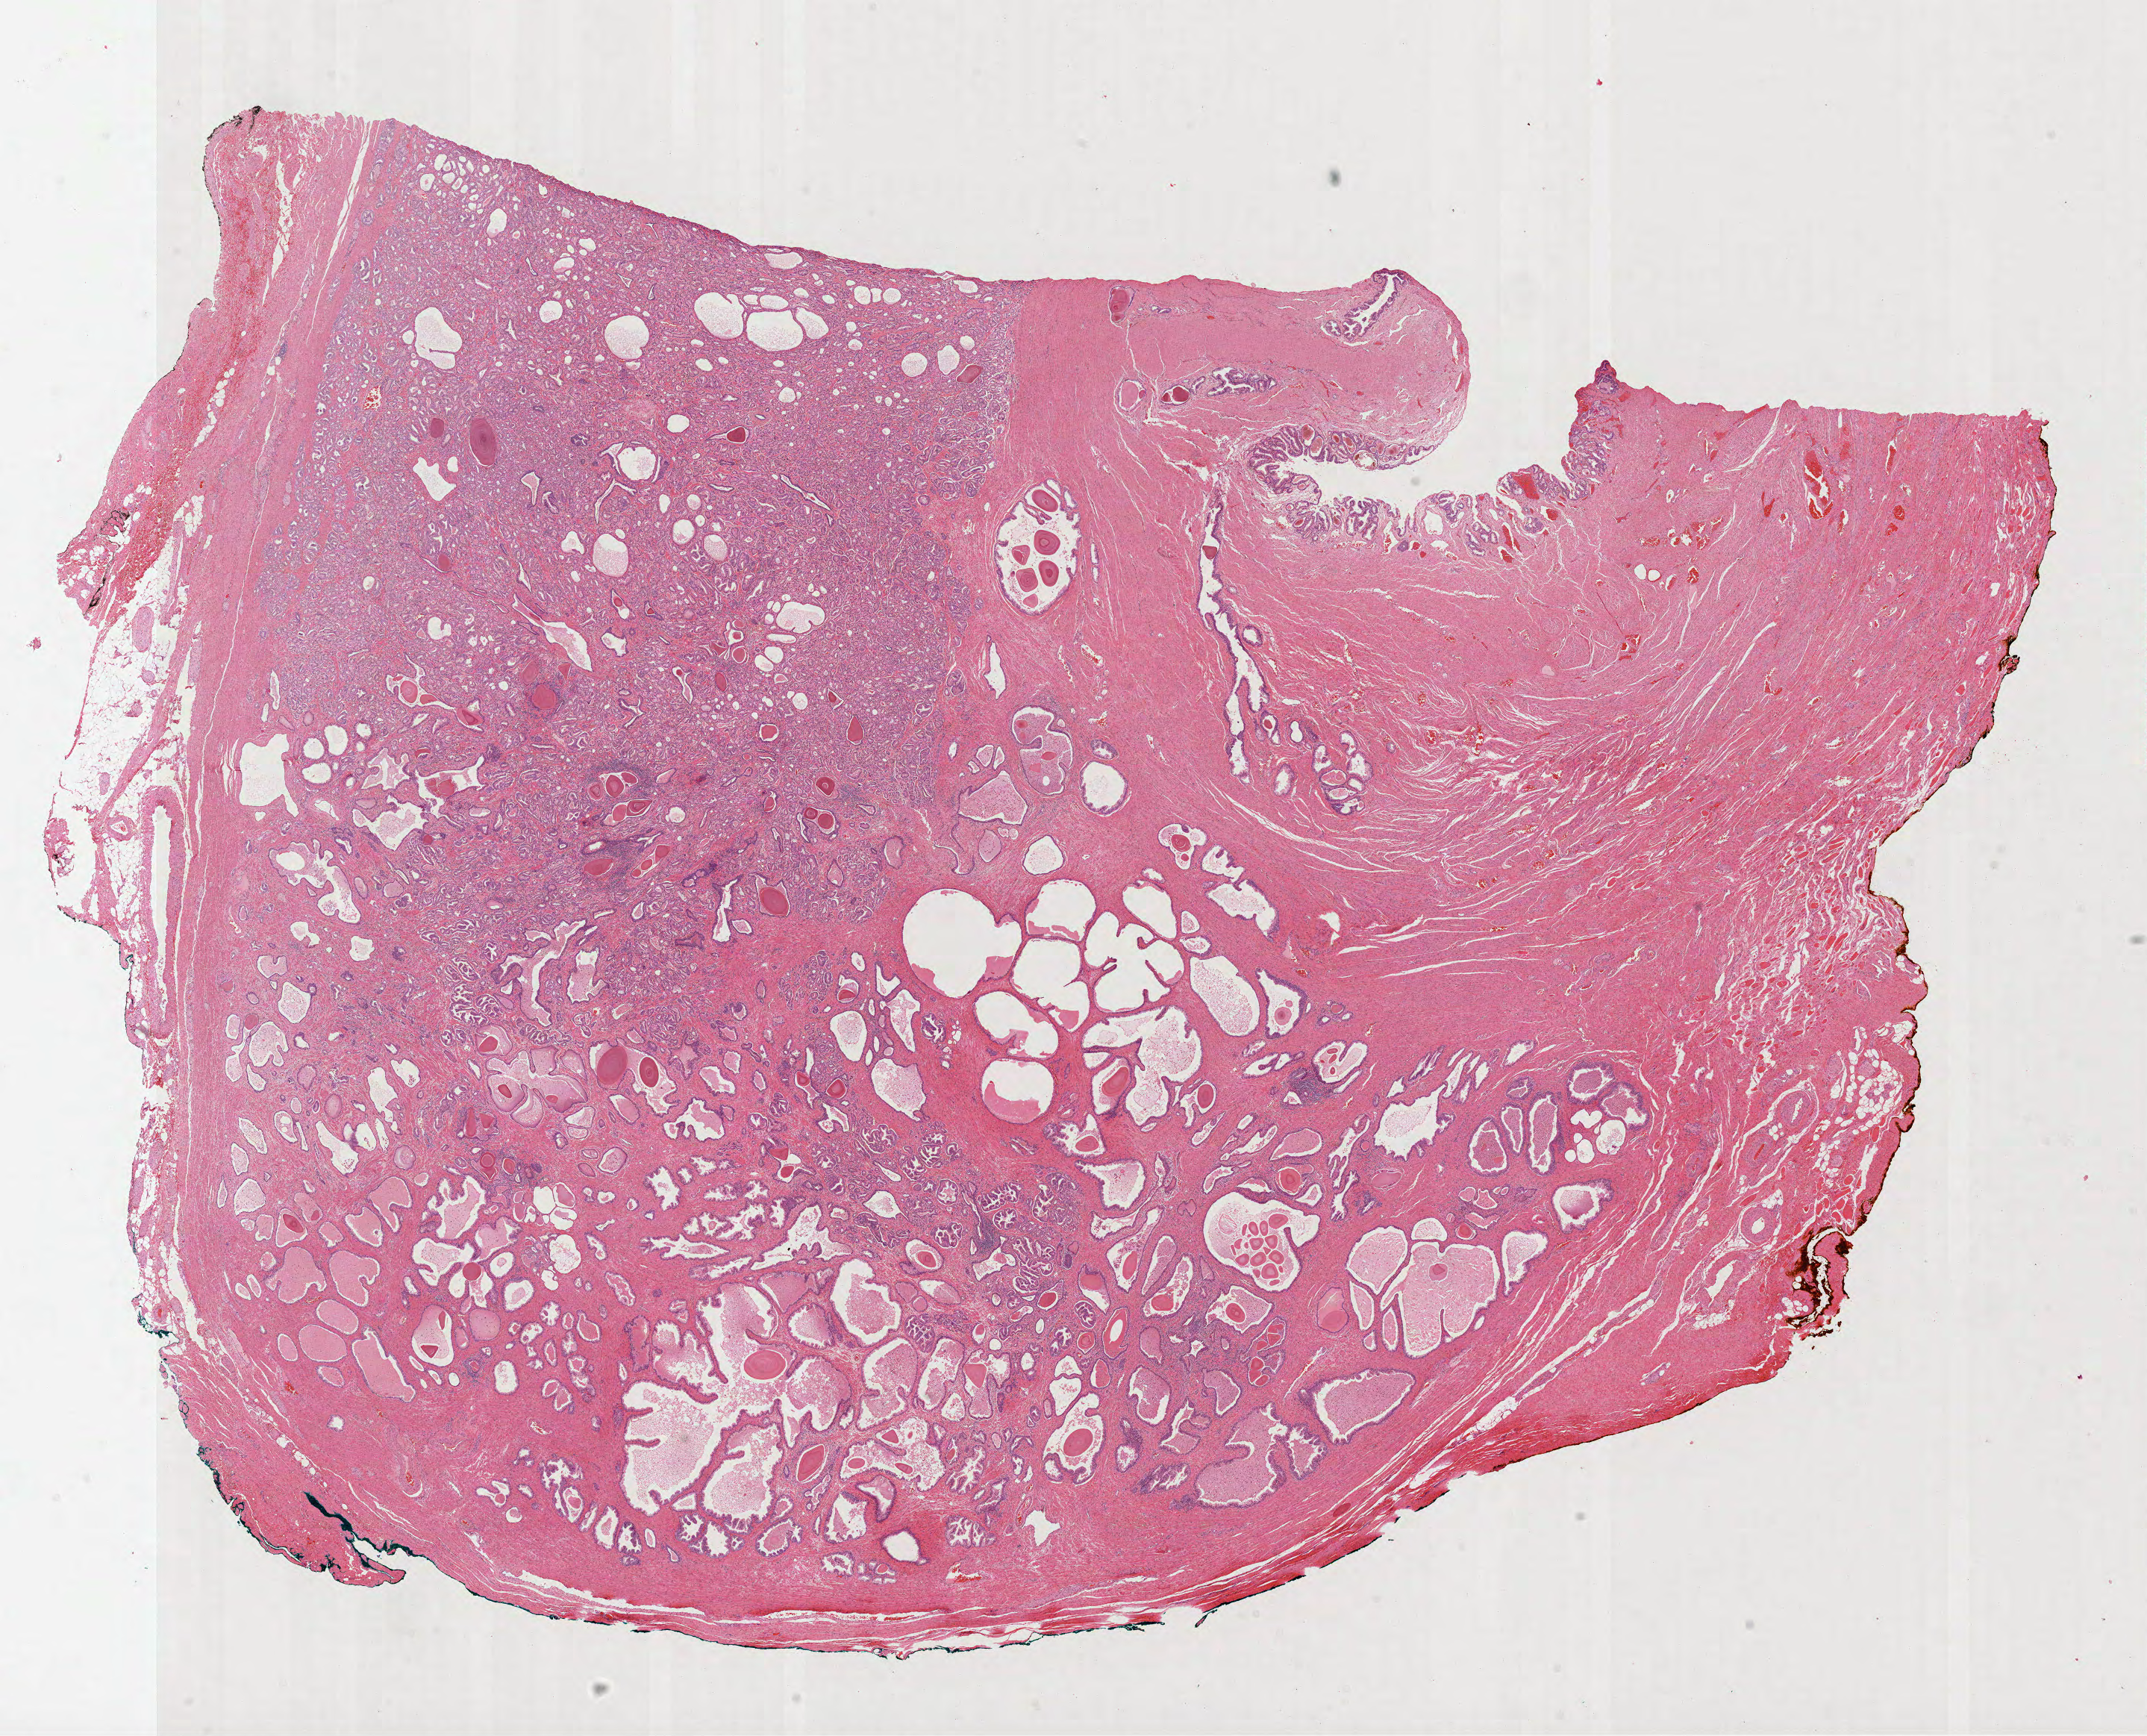
Whole-slide histology image, Hematoxylin and eosin (H&E) stained — low-resolution overview of the scanned area, about 23.2 x 18.8 mm (acquisition: 40x scan); formalin-fixed paraffin-embedded (FFPE) diagnostic section; primary tumour sample from the prostate. Patient: male, age at initial diagnosis 55 years.
Histologic diagnosis: Acinar cell carcinoma (prostate gland).